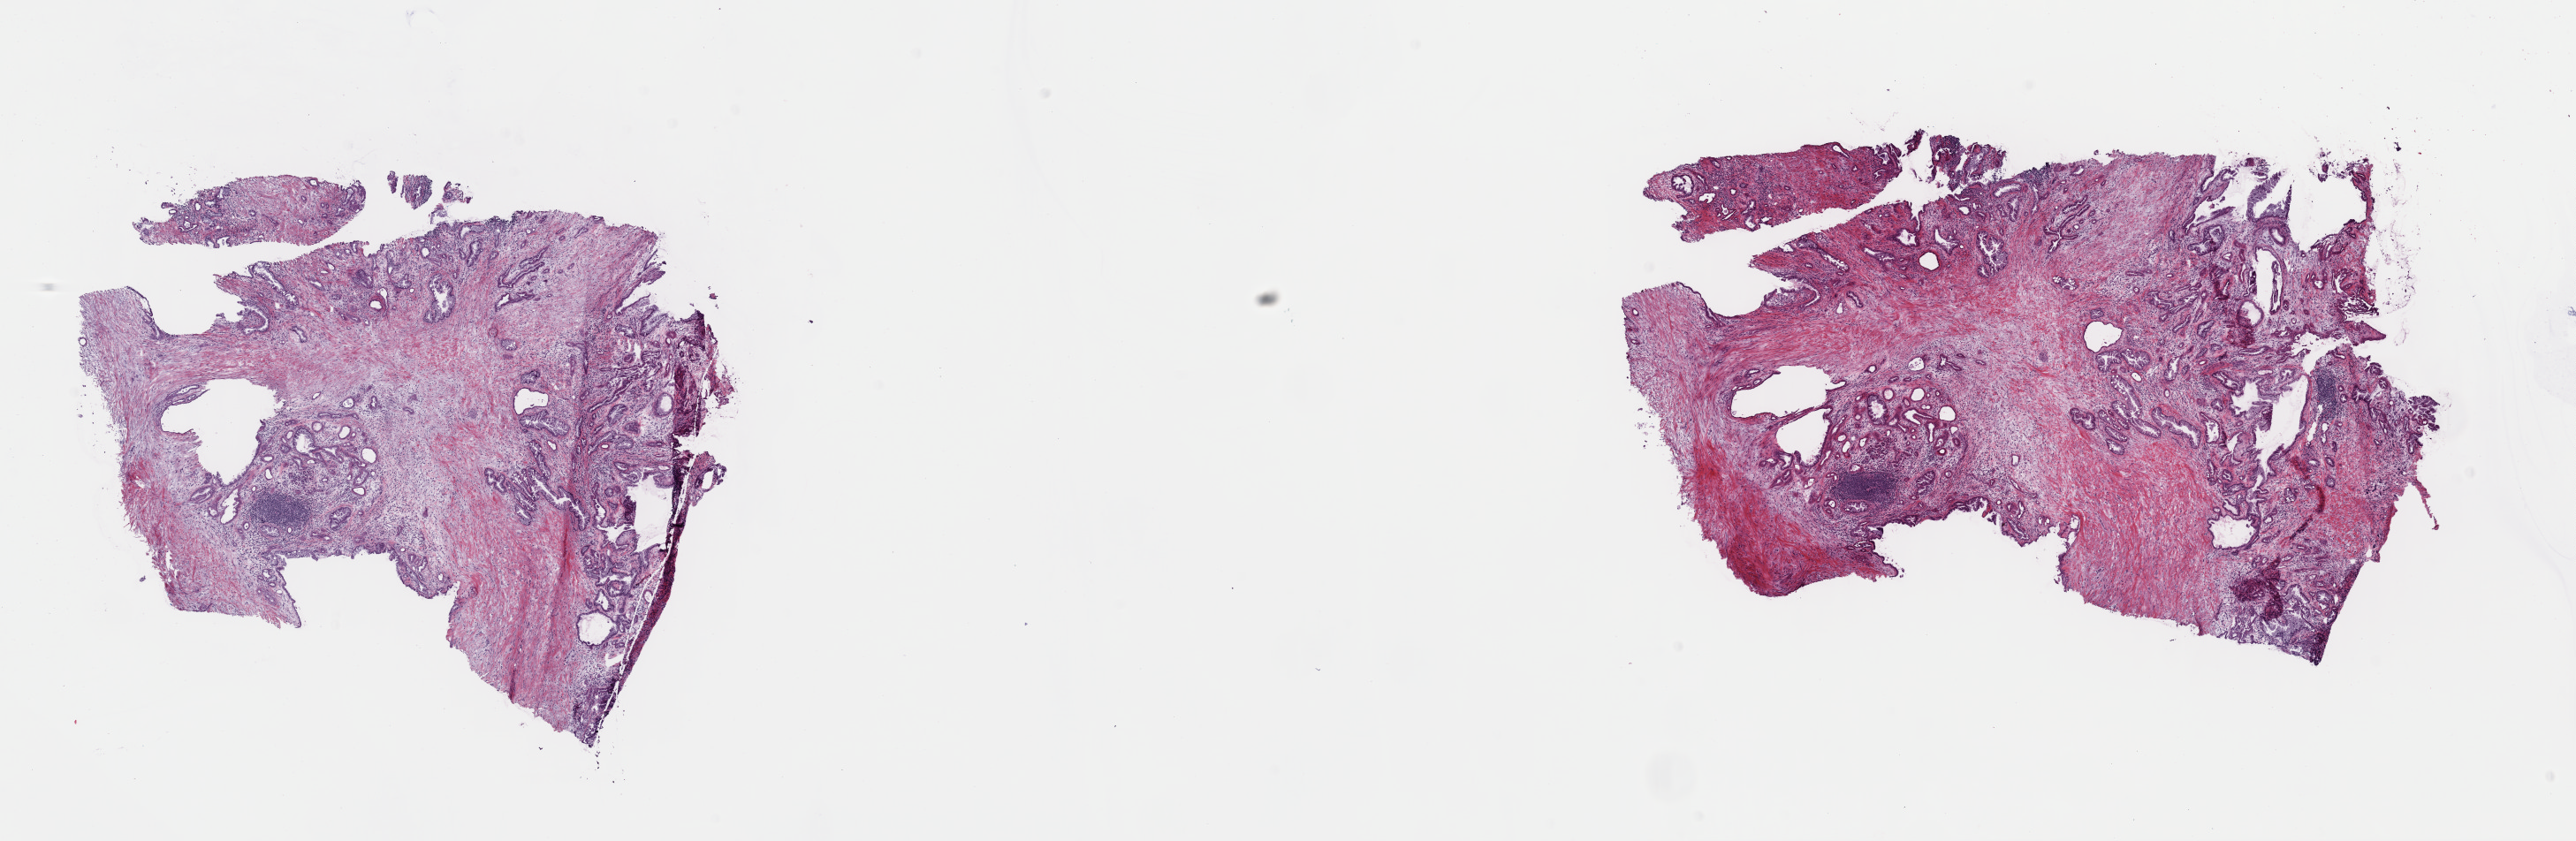
Digitized H&E-stained tissue section (whole slide) — a low-resolution overview of the entire scanned area, about 23.0 x 7.5 mm, frozen section, sample: primary tumour, pancreas. Male, age 77 years at initial diagnosis. Composition of this section per pathologist review: tumour cells 5%, tumour nuclei 5%.
Diagnosis: Infiltrating duct carcinoma, NOS (head of pancreas).